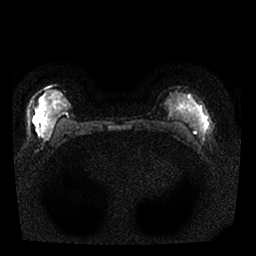
Breast MRI, one axial slice. Slice 12 of 25 in the series (ordered by position). Diffusion-weighted series; image 2 of 4 stored at this slice position (different b-values; order by instance number). 1.5 T. 4 mm slice thickness. 256 × 256 image matrix, field of view 310 × 310 mm. Female patient.
Outlined on this slice (manually delineated by an expert):
- tumour on diffusion-weighted imaging: bounding box [x1, y1, x2, y2] px = [38, 128, 53, 138]